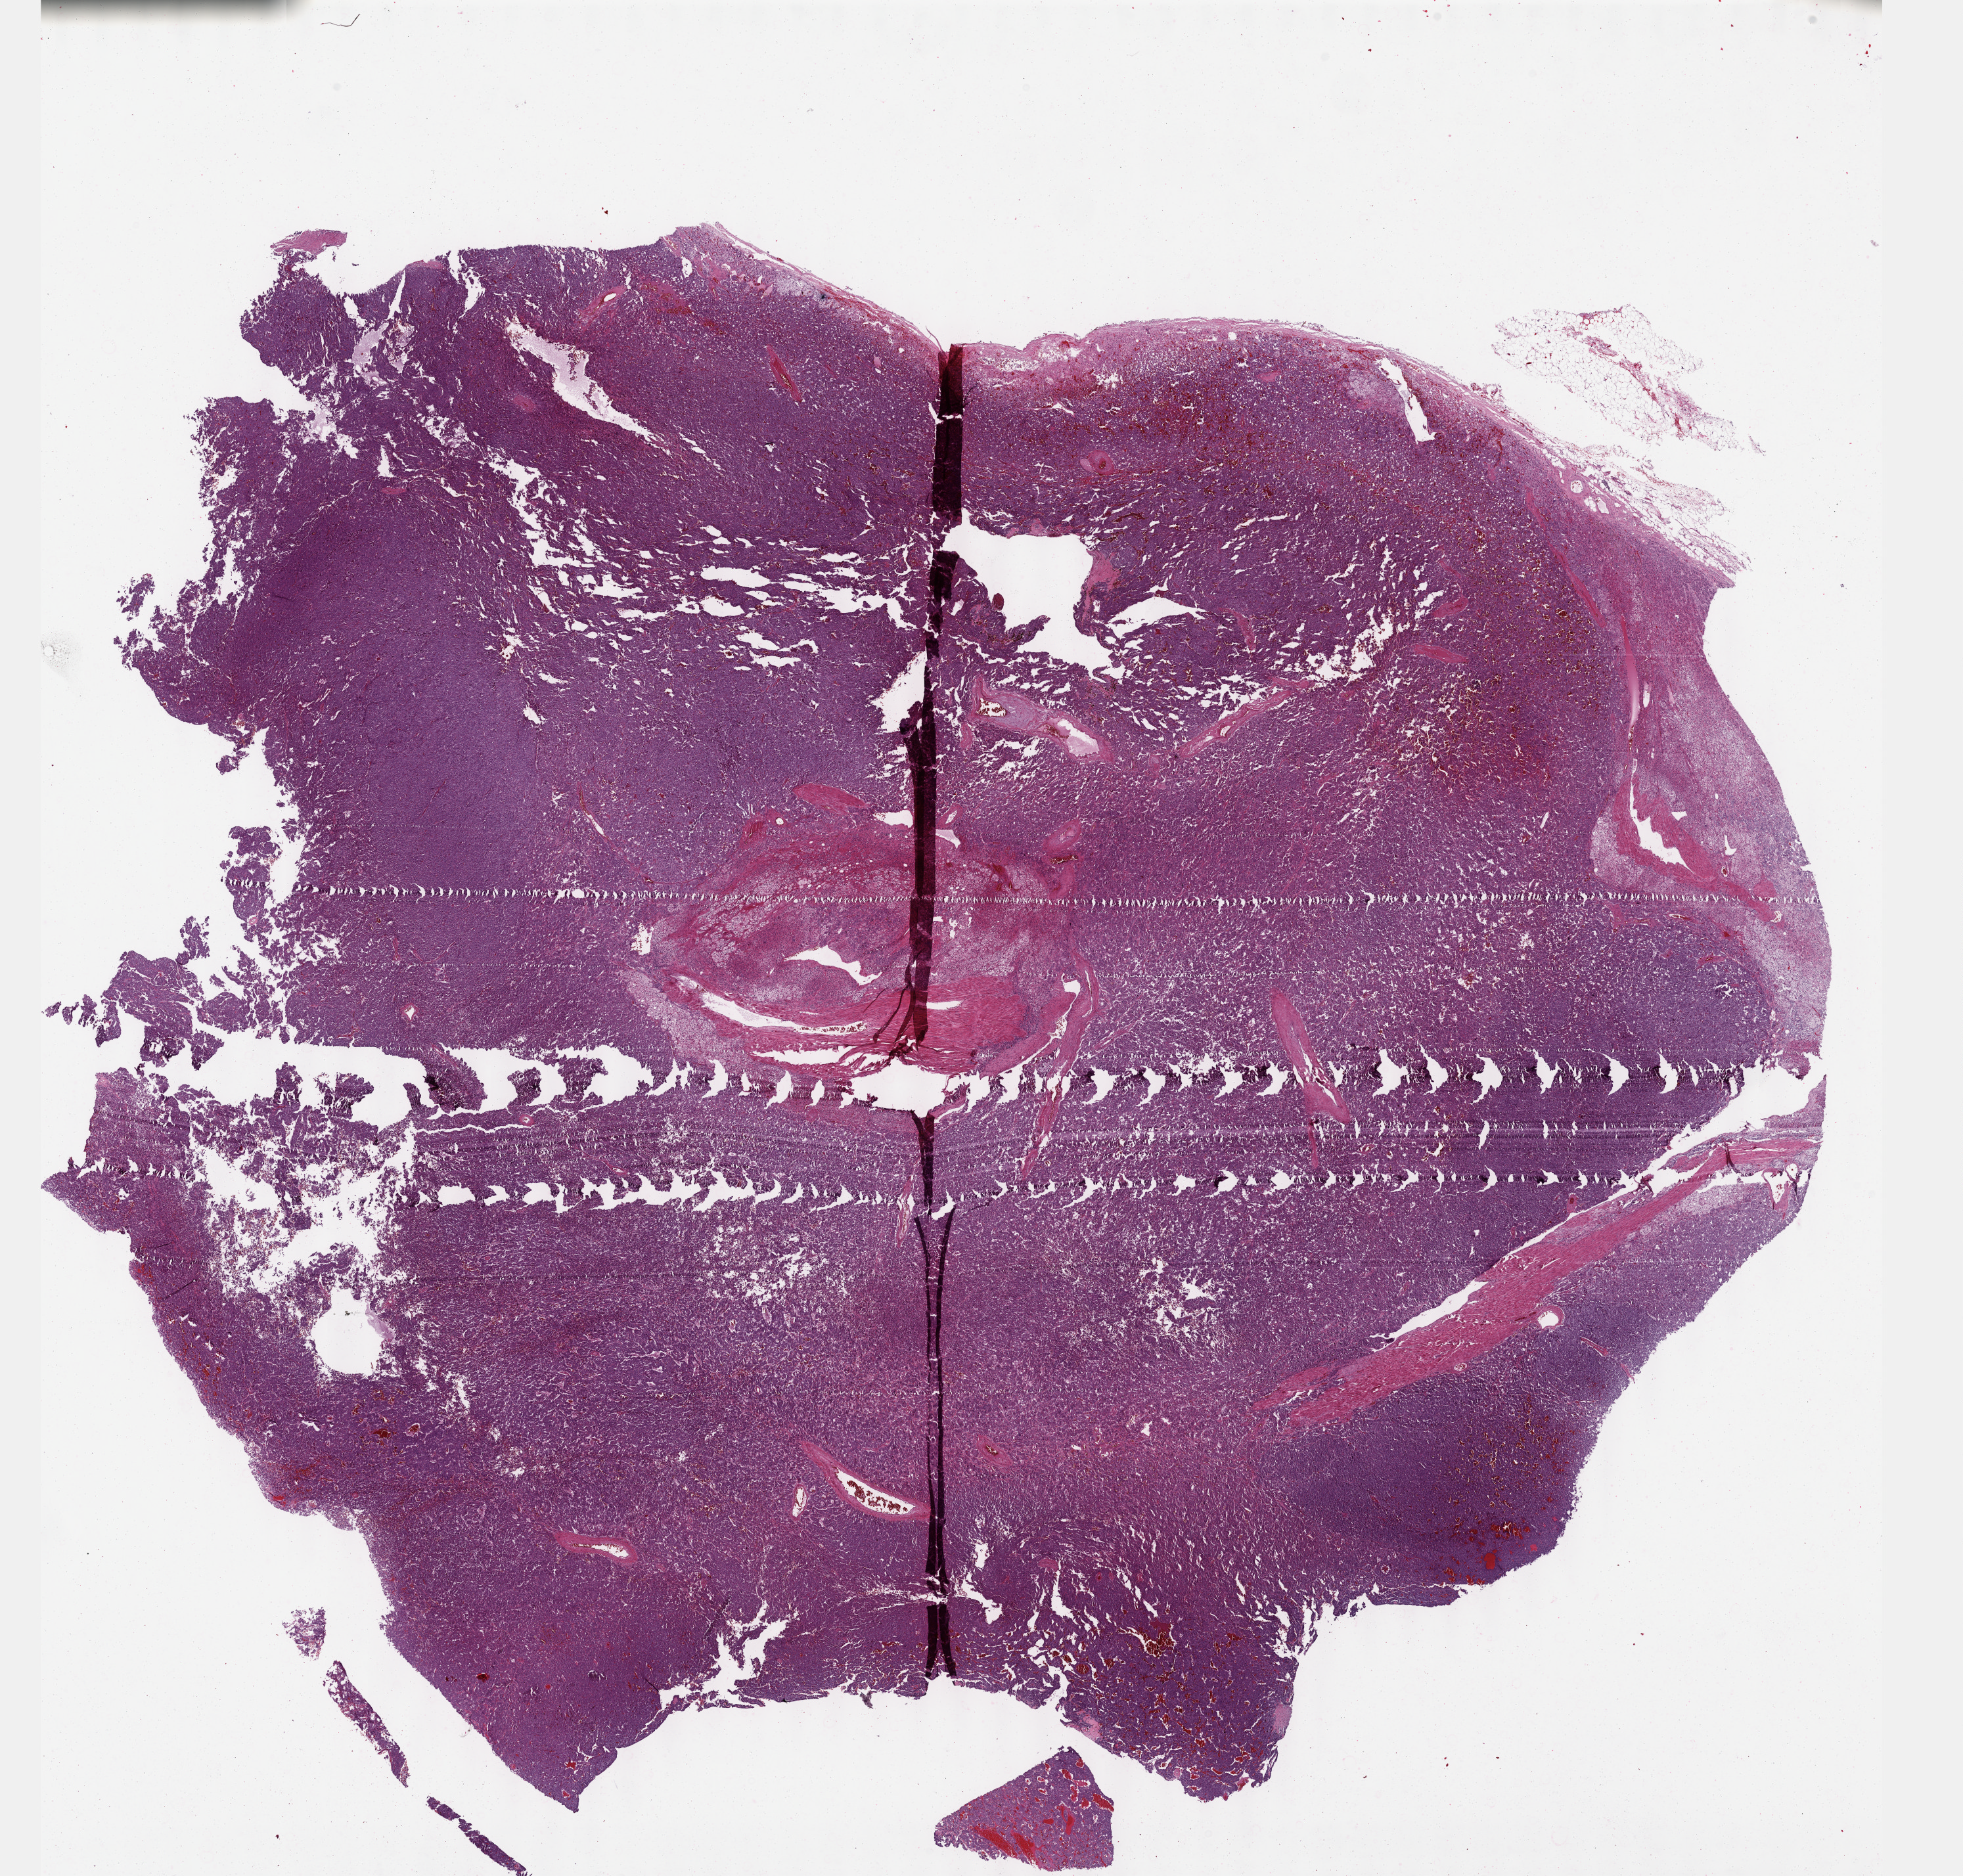
Digitized Hematoxylin and eosin (H&E) stained tissue section (whole slide) — shown as a low-resolution overview of the whole scanned area (about 24.1 x 23.1 mm), formalin-fixed paraffin-embedded (FFPE) diagnostic section, primary tumour sample from the adrenal gland. Patient: female, age at initial diagnosis 82 years.
Laterality: left. Pathologic diagnosis: Pheochromocytoma, NOS.